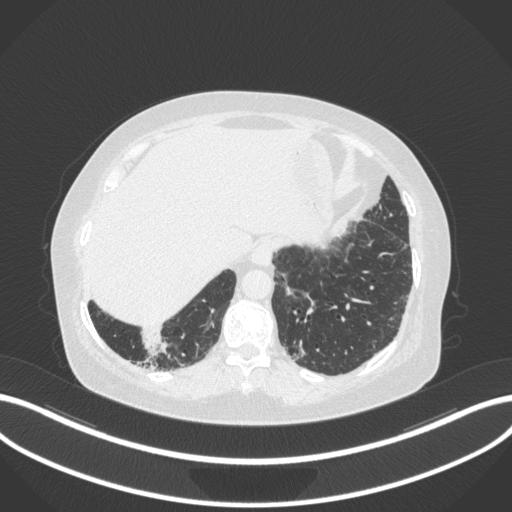
Chest CT, one axial slice. Slice 18 of 303 in the series (ordered by position). Reconstruction kernel B31f. Lung window (W 1500 / L -600 HU). 512 × 512 image matrix, field of view 400 × 400 mm. Patient: female, 65 years. Case-level facts recorded for this patient, not image findings: clinical TNM (as recorded): T2b N1 M0; histopathological grade: G1.
Outlined on this slice (bounding box drawn by a radiologist):
- lung tumour (recorded histology: adenocarcinoma): box from (x=138, y=328) to (x=174, y=359) px